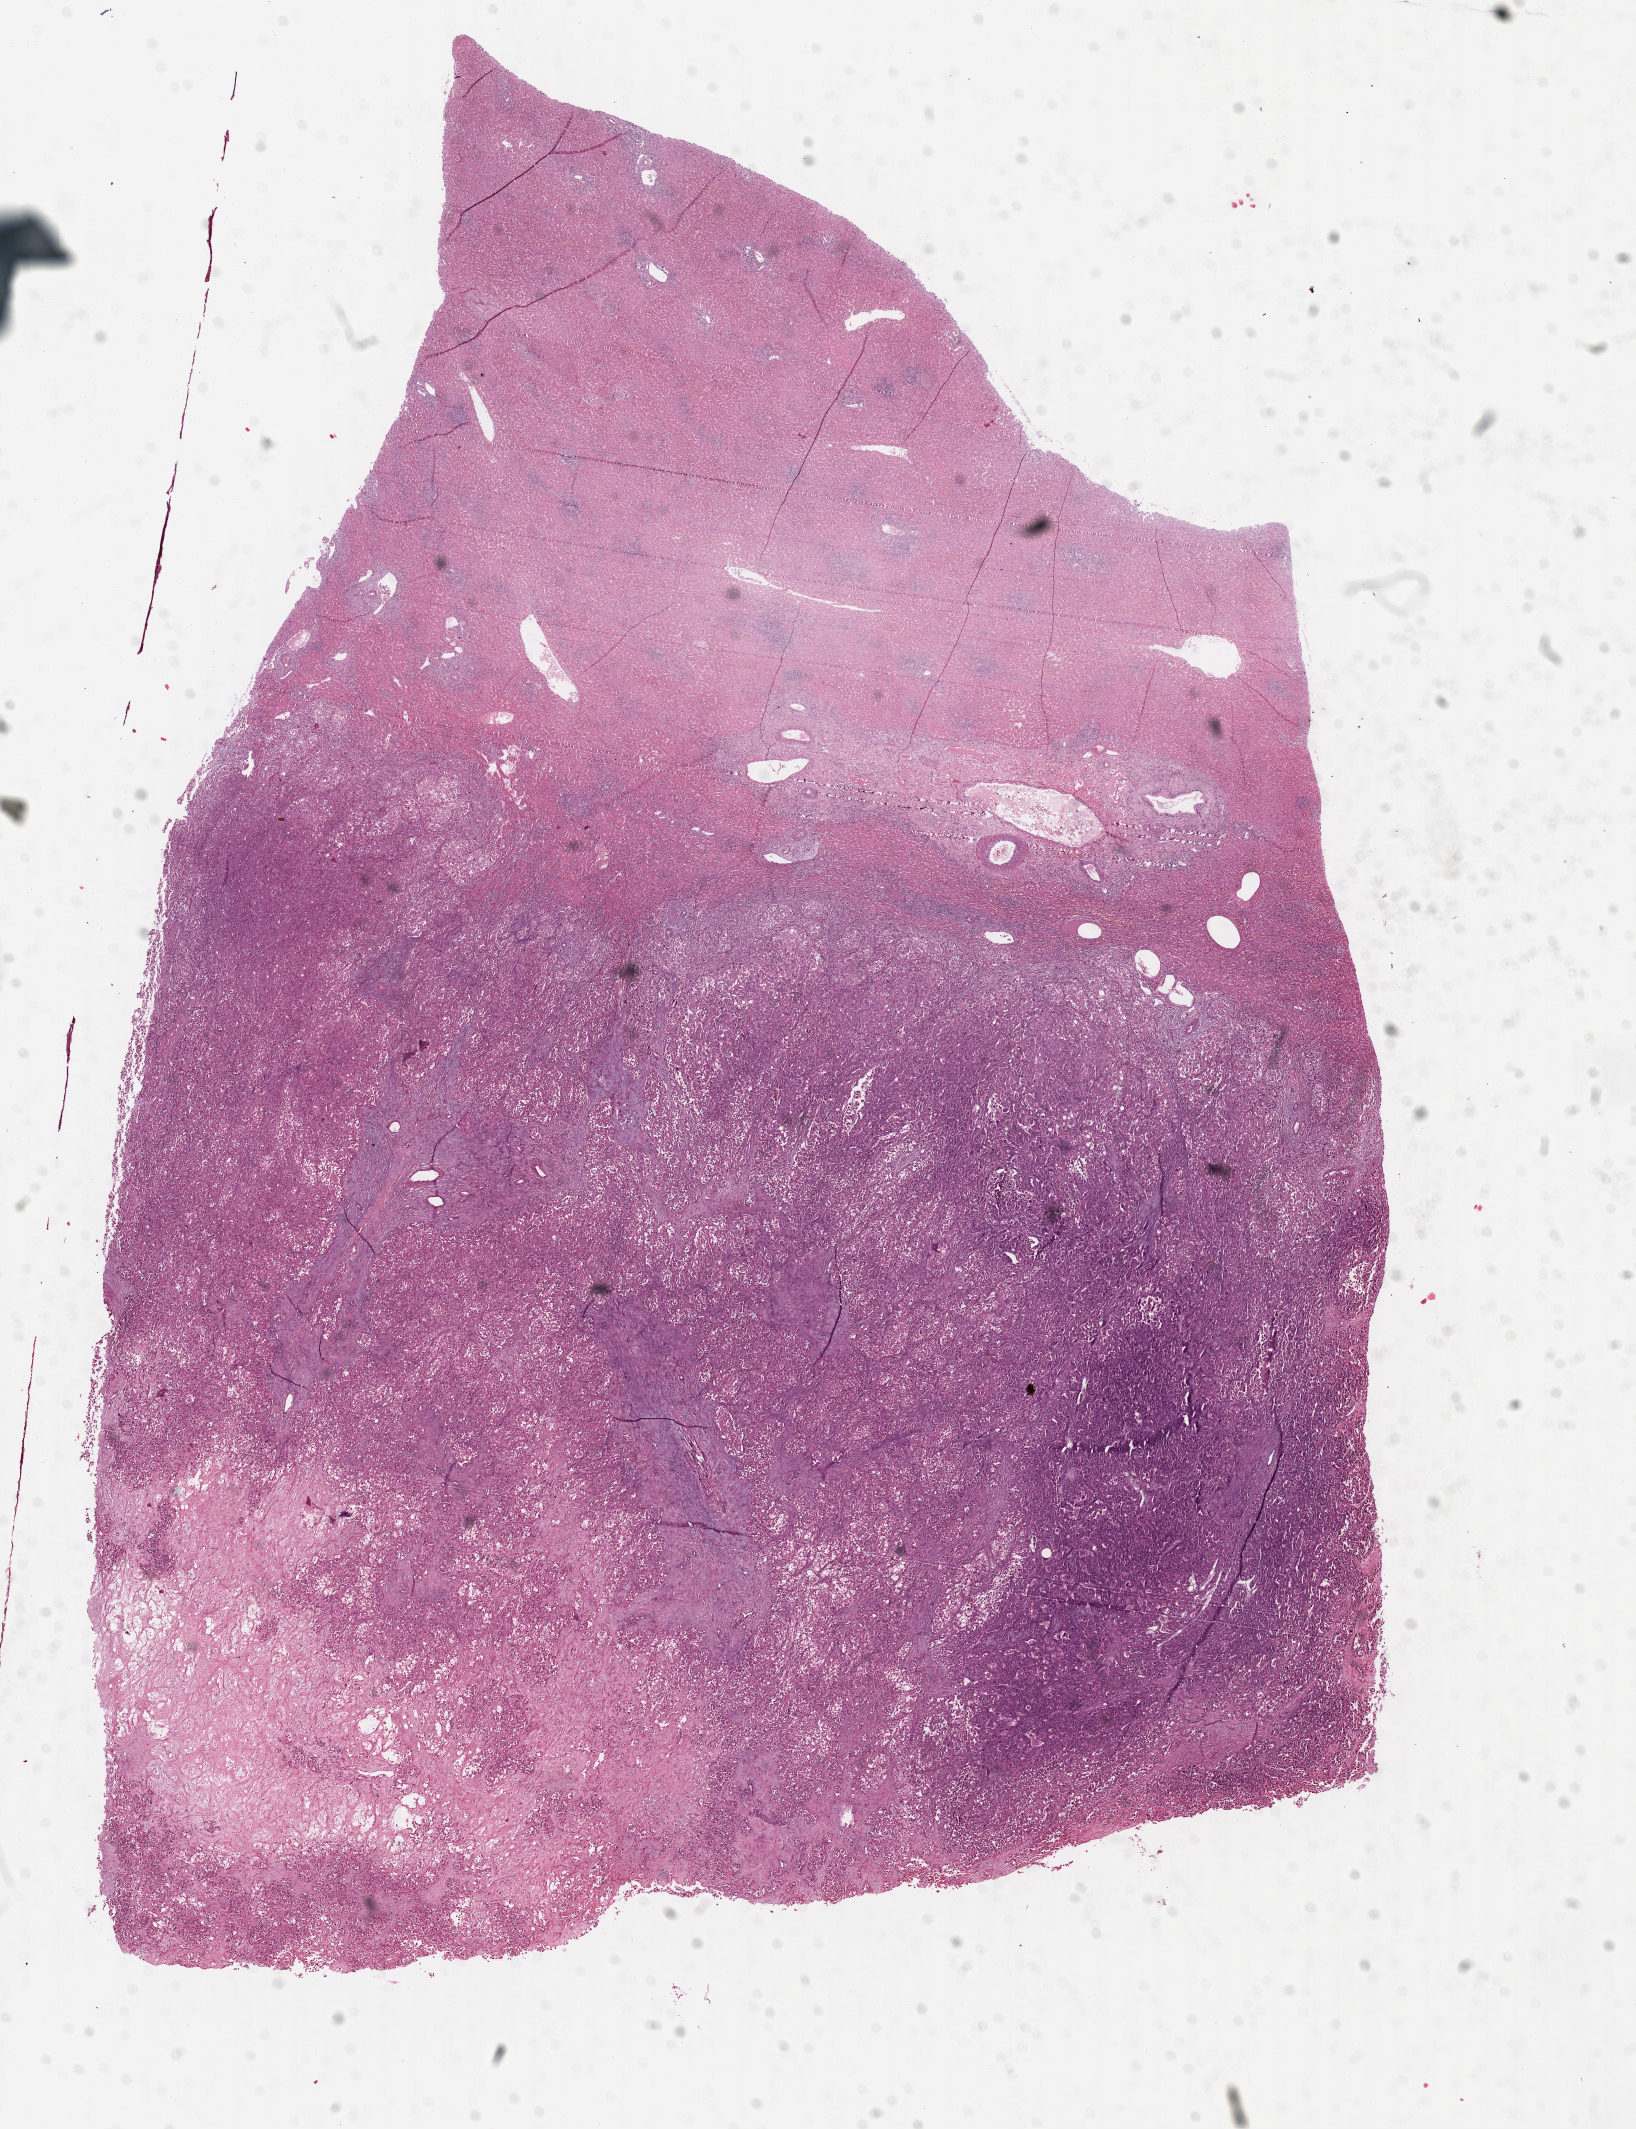
Digitized H&E-stained tissue section (whole slide), a low-resolution overview of the entire scanned area, about 12.9 x 16.7 mm (slide scanned at 40x). Formalin-fixed paraffin-embedded (FFPE) diagnostic section. Sample: primary tumour, liver. Female, age 61 years at initial diagnosis. Histologic grade: G1 (well differentiated).
Pathologic diagnosis: Hepatocellular carcinoma, NOS. AJCC pathologic stage: IIIC.